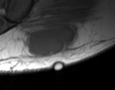
MRI of an extremity soft-tissue mass, one axial slice. Position 15 of 35 along the scan axis. MR volume resampled by the dataset authors to the PET/CT grid (not the native acquisition matrix). 115 × 90 image matrix. Male patient. From the clinical record (not read from this slice): histological type: pleiomorphic leiomyosarcoma; grade: high; site of the primary tumour: left buttock.
Outlined on this slice (expert contour drawn on MRI and transferred to this co-registered scan by the dataset authors):
- gross tumour volume including surrounding oedema: bounding box (x1, y1, x2, y2) in pixels: (24, 21, 81, 58)
- gross tumour volume (mass): (28, 23, 79, 58)